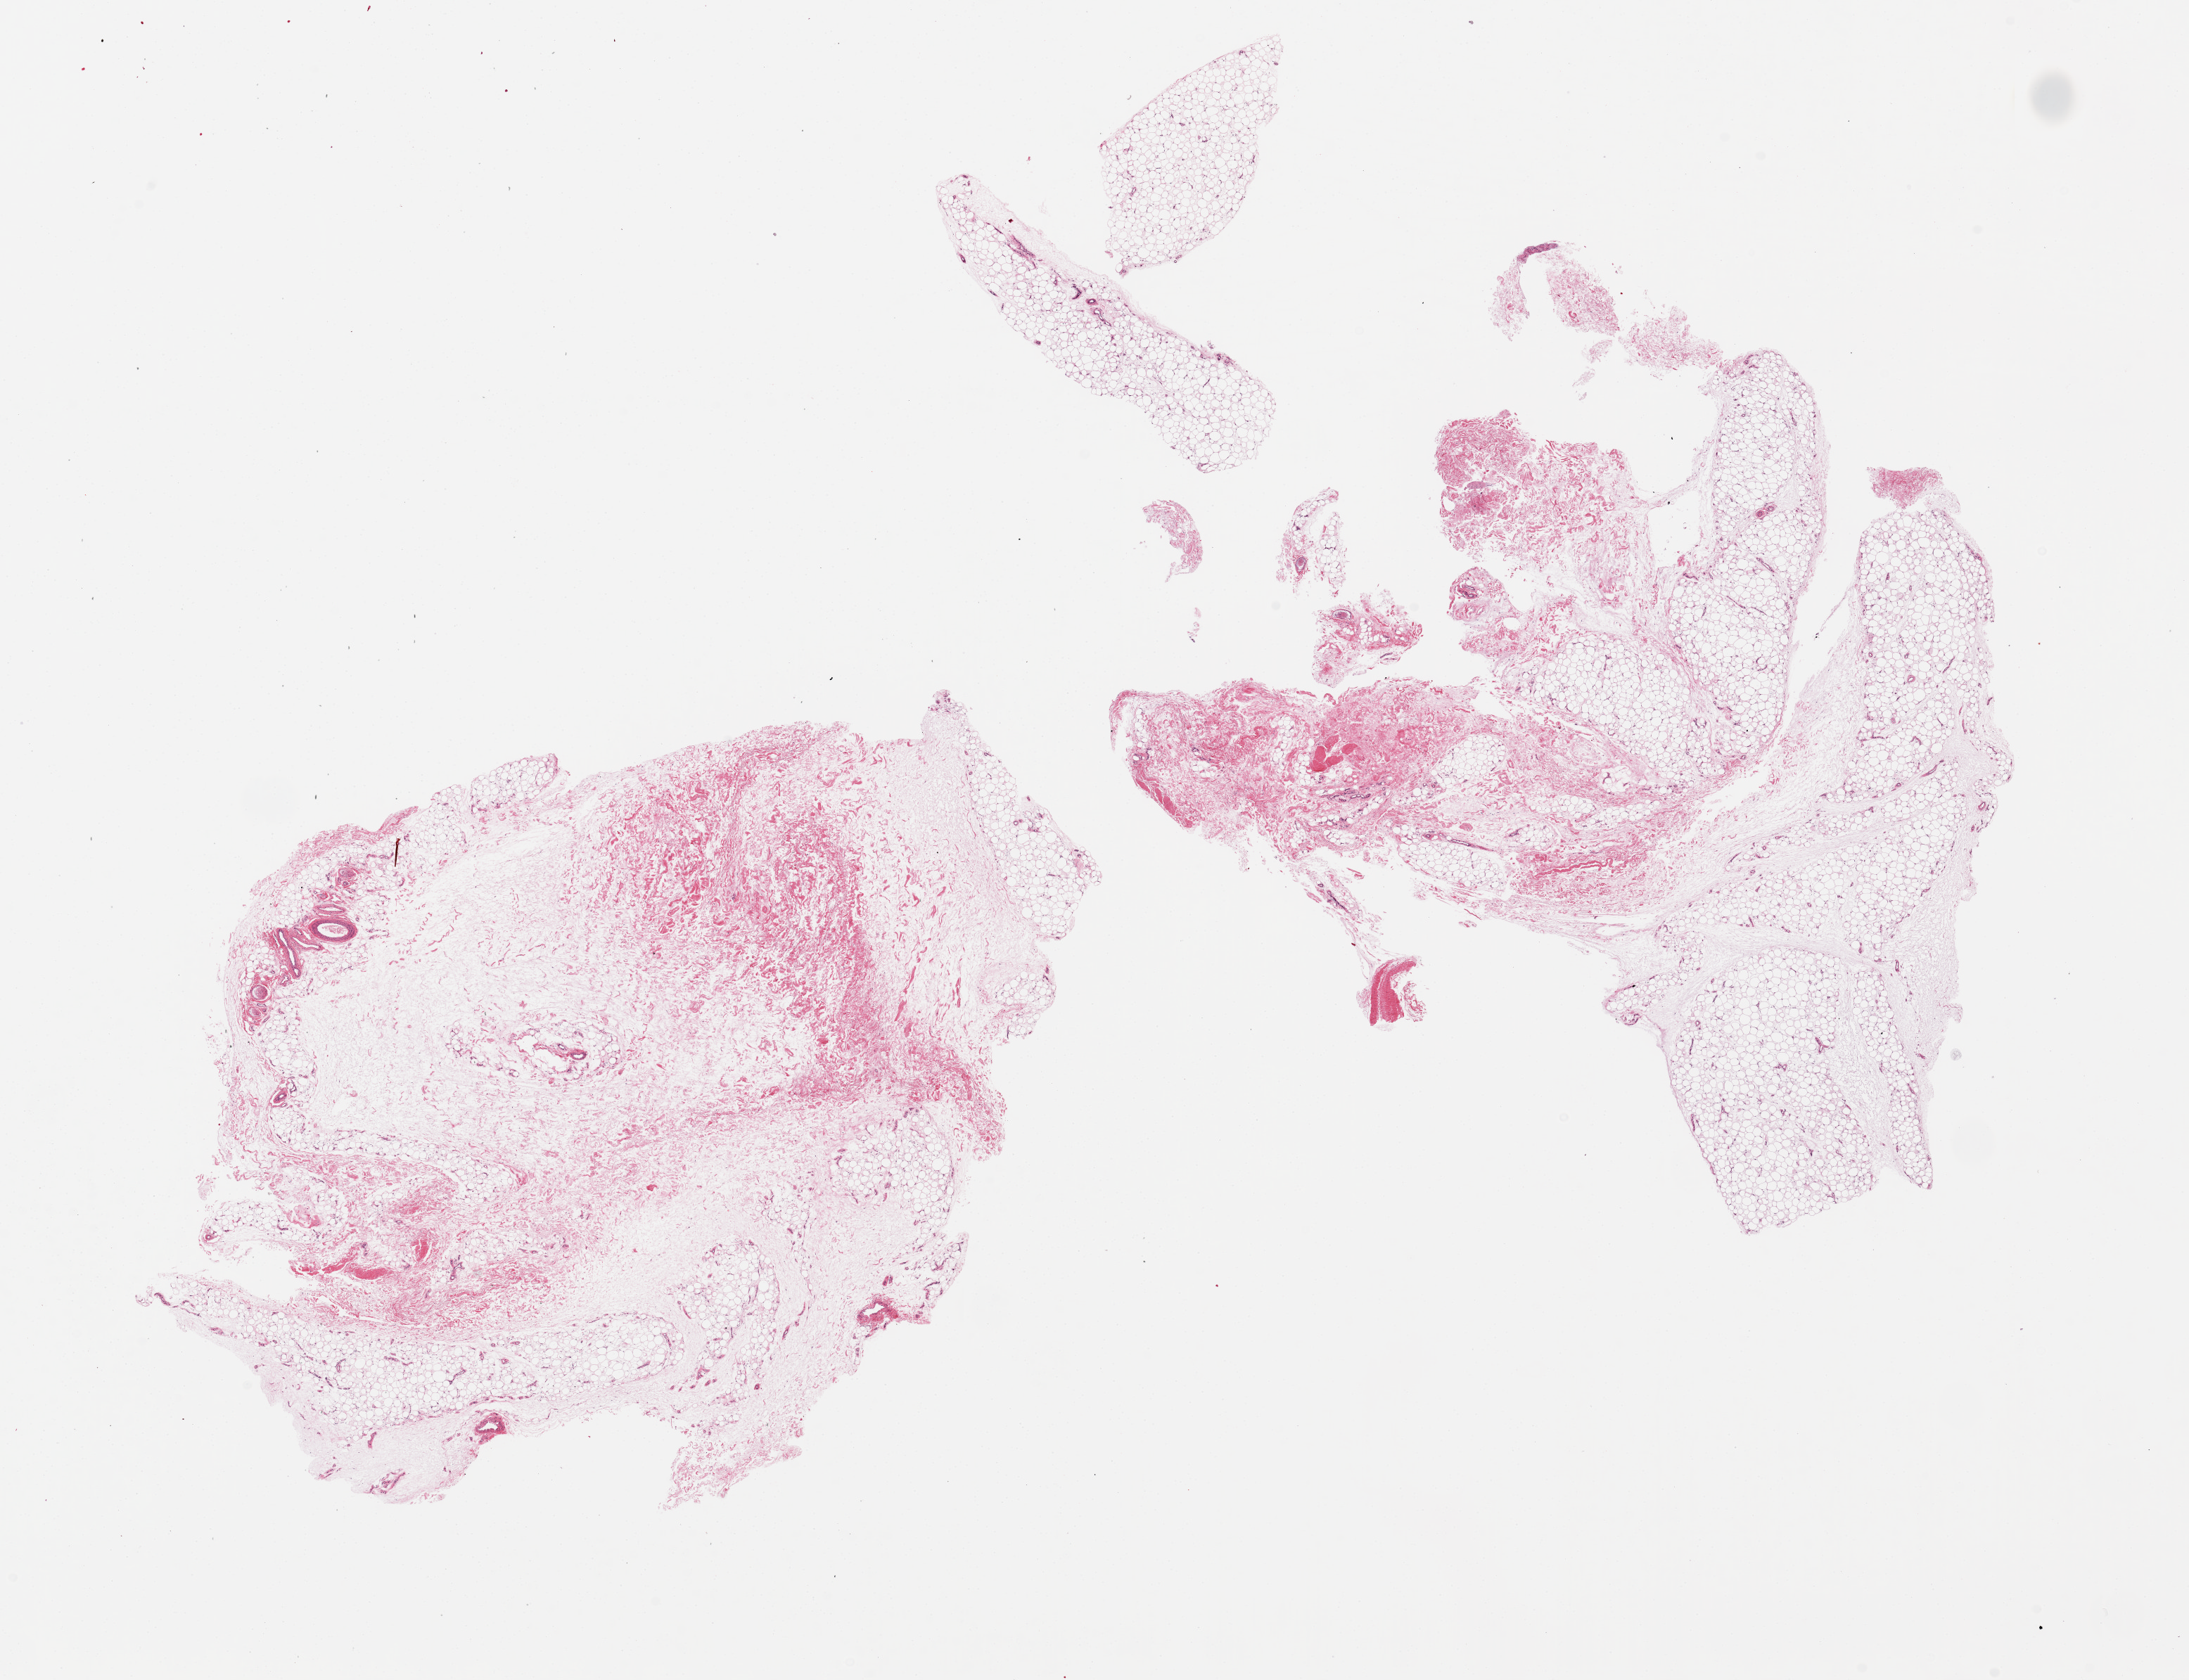
Hematoxylin and eosin (H&E) whole-slide image — whole scanned area (about 24.6 x 18.9 mm, from a 20x scan) shown as a low-resolution overview, PAXgene-fixed paraffin-embedded (PFPE) section, section of adipose tissue (target tissue), donor tissue sample.
- review note (as recorded): 2 pieces, 16x9 & 11x9mm; 20% fibroadipose, rest is adipose